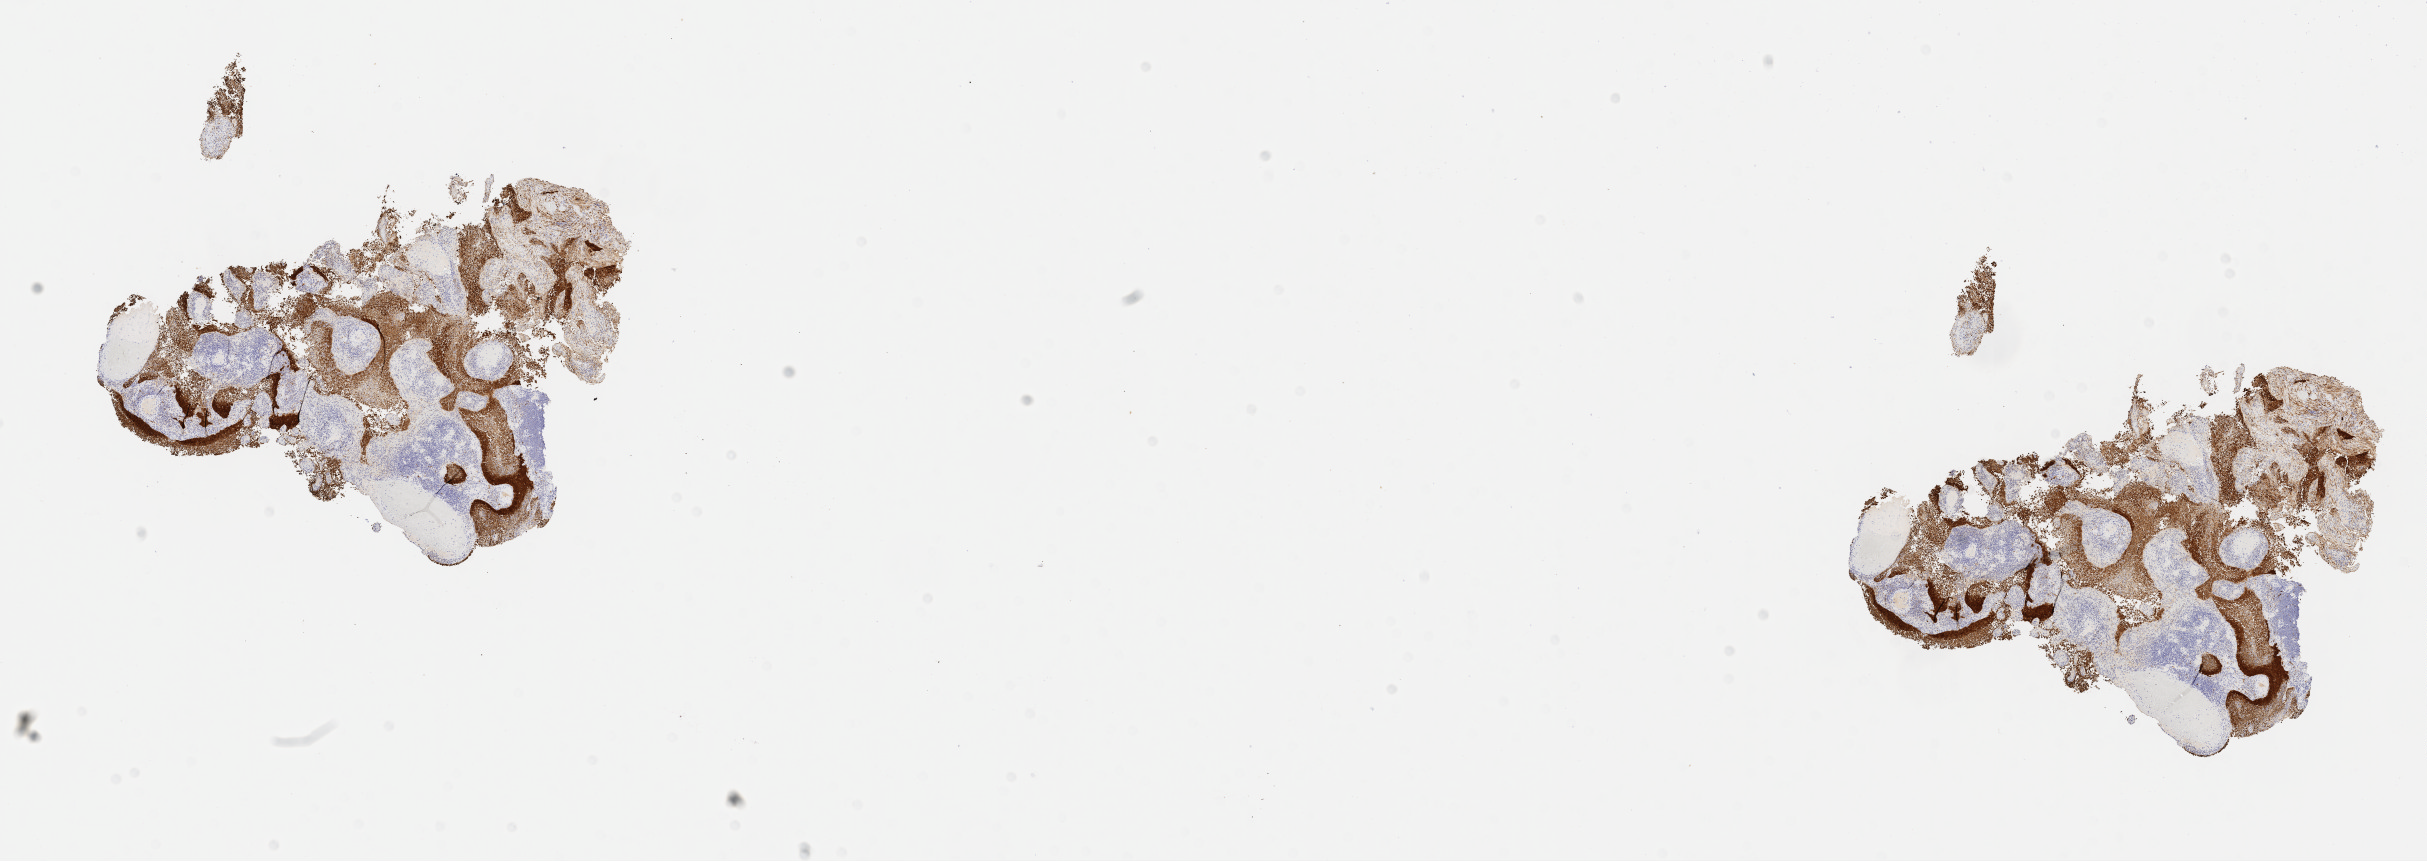
Whole-slide image, immunohistochemical stain for p16 (p16INK4a), shown as a low-resolution overview of the whole scanned area (about 19.6 x 7.0 mm); specimen: tumor tissue; site: cervix. Patient: female, 52 years old.
Diagnosis: Squamous cell carcinoma, large cell, nonkeratinizing, NOS.